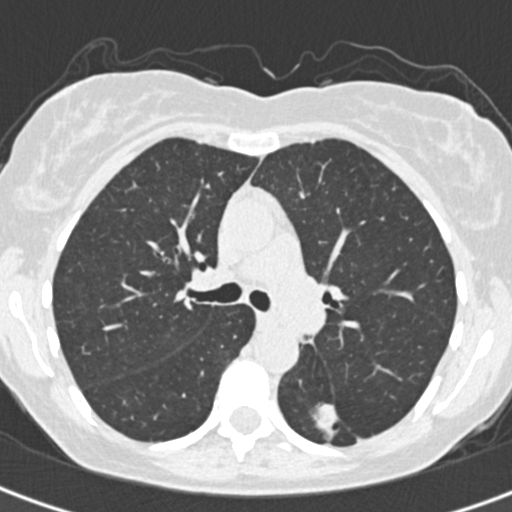
Low-dose screening chest CT, one axial slice; slice 212 of 328 in the series (ordered by position); reconstruction kernel B30f; 120 kVp; lung window (W 1500 / L -600 HU); 1 mm slice thickness; 512 × 512 image matrix, field of view 284 × 284 mm.
Annotated regions visible in this slice (manually delineated by an expert):
- lesion 1 (tumor, lower lobe of left lung): bounding box <313,404,338,438> (left, top, right, bottom; pixels)